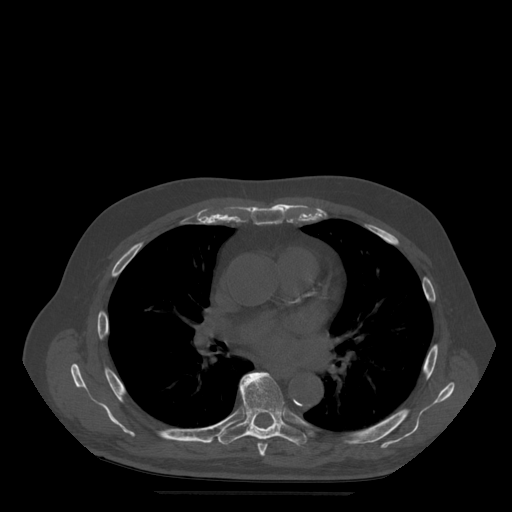
CT including the spine, one axial slice; position 338 of 522 along the scan axis; bone window (W 1800 / L 400 HU); 1.25 mm slice thickness; 512 × 512 image matrix, field of view 420 × 420 mm. Patient age 72 years. From the clinical record (not read from this slice): primary cancer: prostate.
Outlined on this slice (semi-automatically segmented with operator editing):
- T6 vertebra: box from (x=241, y=373) to (x=268, y=457) px
- T7 vertebra: (x=216, y=373)–(x=307, y=446)